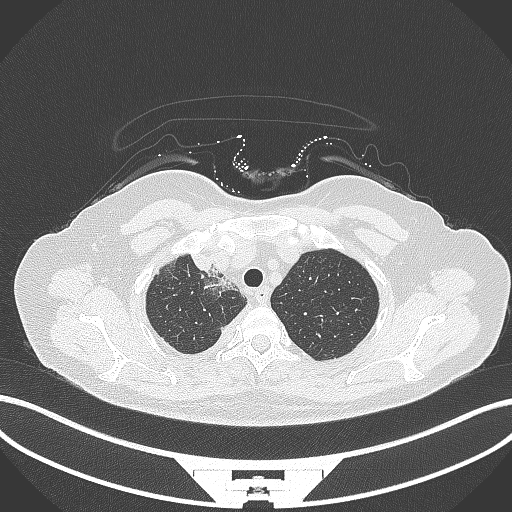
Chest CT, one axial slice. Slice 263 of 305 in the series (ordered by position). 120 kVp. Lung window (W 1500 / L -600 HU). 512 × 512 image matrix, field of view 400 × 400 mm. Female patient, age 52 years. Case-level facts recorded for this patient, not image findings: clinical TNM (as recorded): T3 N1 M1.
Annotated regions visible in this slice (bounding box drawn by a radiologist):
- lung tumour (recorded histology: adenocarcinoma): bounding box [x1, y1, x2, y2] px = [186, 250, 215, 276]